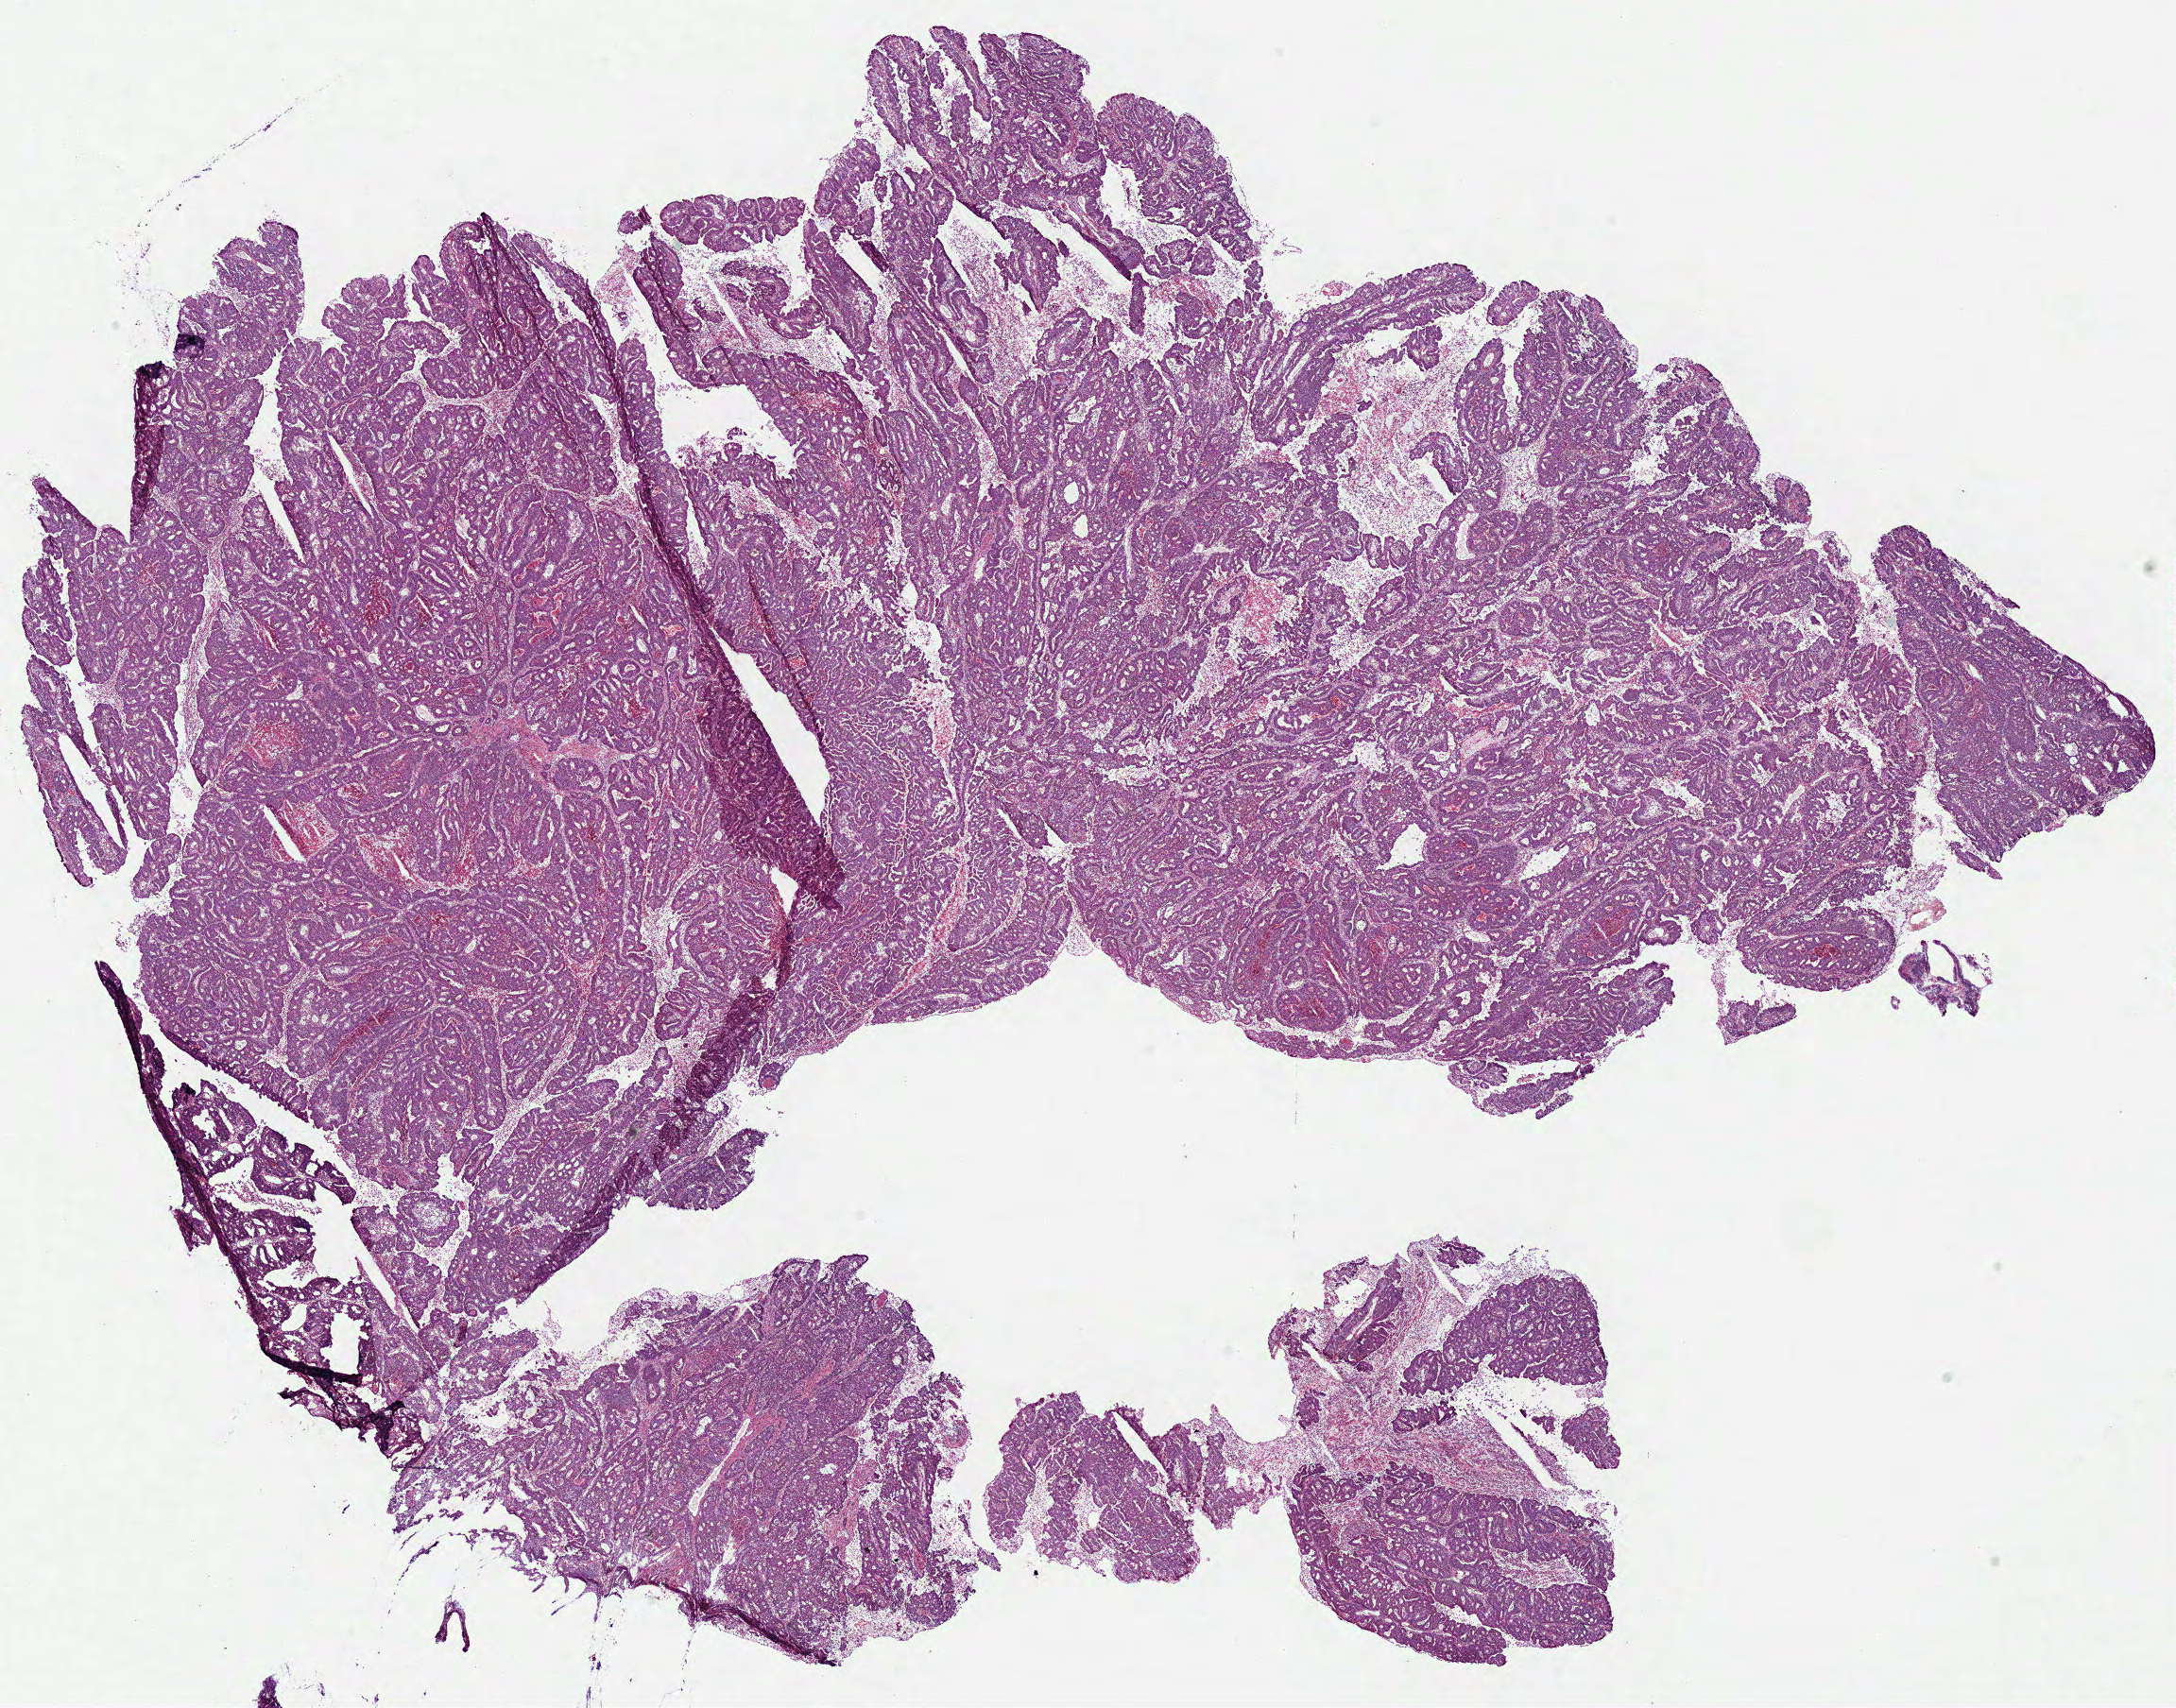
Digitized H&E tissue section (whole slide), low-resolution overview of the scanned area, about 18.1 x 14.2 mm (from a 40x scan); frozen section; primary tumour sample from the colon. Female patient; age at initial diagnosis 77 years. Pathologist review of this section (percent, as recorded): tumour cells 84%, tumour nuclei 85%, normal cells 0%, stromal cells 8%, necrosis 8%.
Histologic diagnosis: Adenocarcinoma, NOS (ascending colon). Lymph nodes positive (case pathology): 0 of 28 examined. AJCC pathologic stage: I.